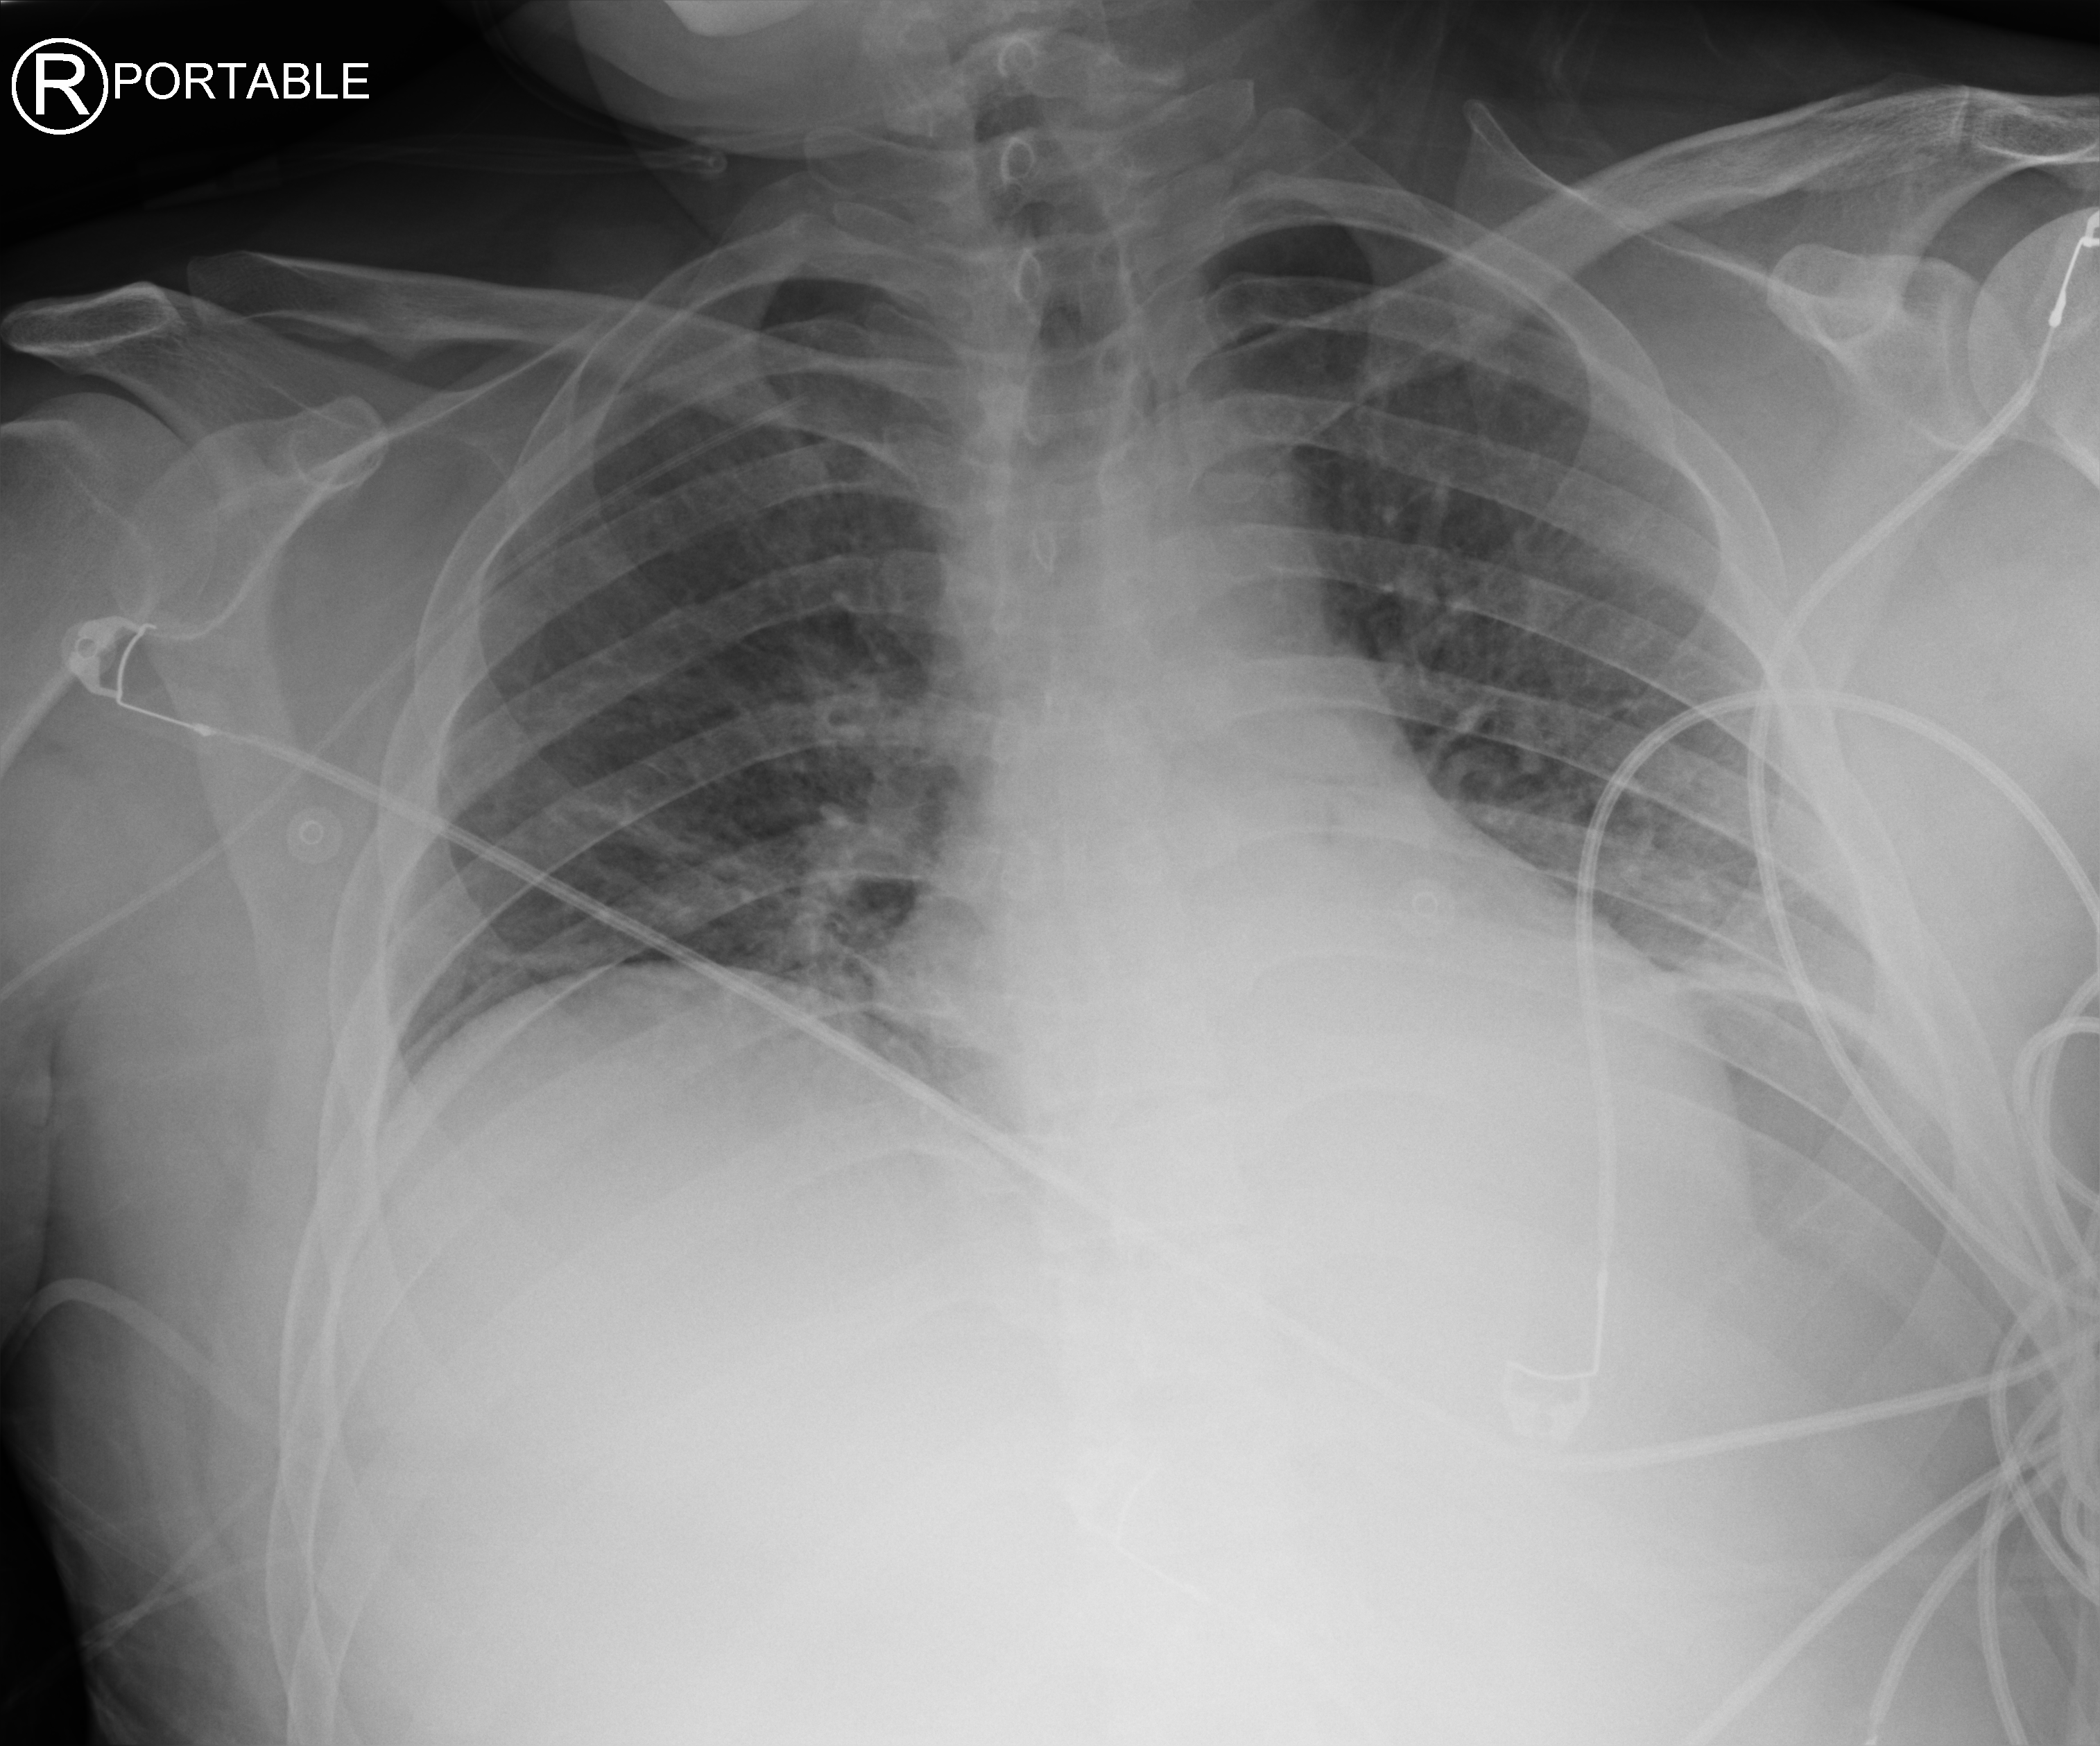
Bedside chest radiograph (computed radiography), anteroposterior (AP) projection. Patient hospitalised with COVID-19; male, aged 18–59 years.
From the hospital-stay record, not from the radiograph (when in the stay this image was taken is not recorded): smoking status (admission record): current; admitted to intensive care during this hospital stay: yes; mechanically ventilated during this hospital stay: yes.